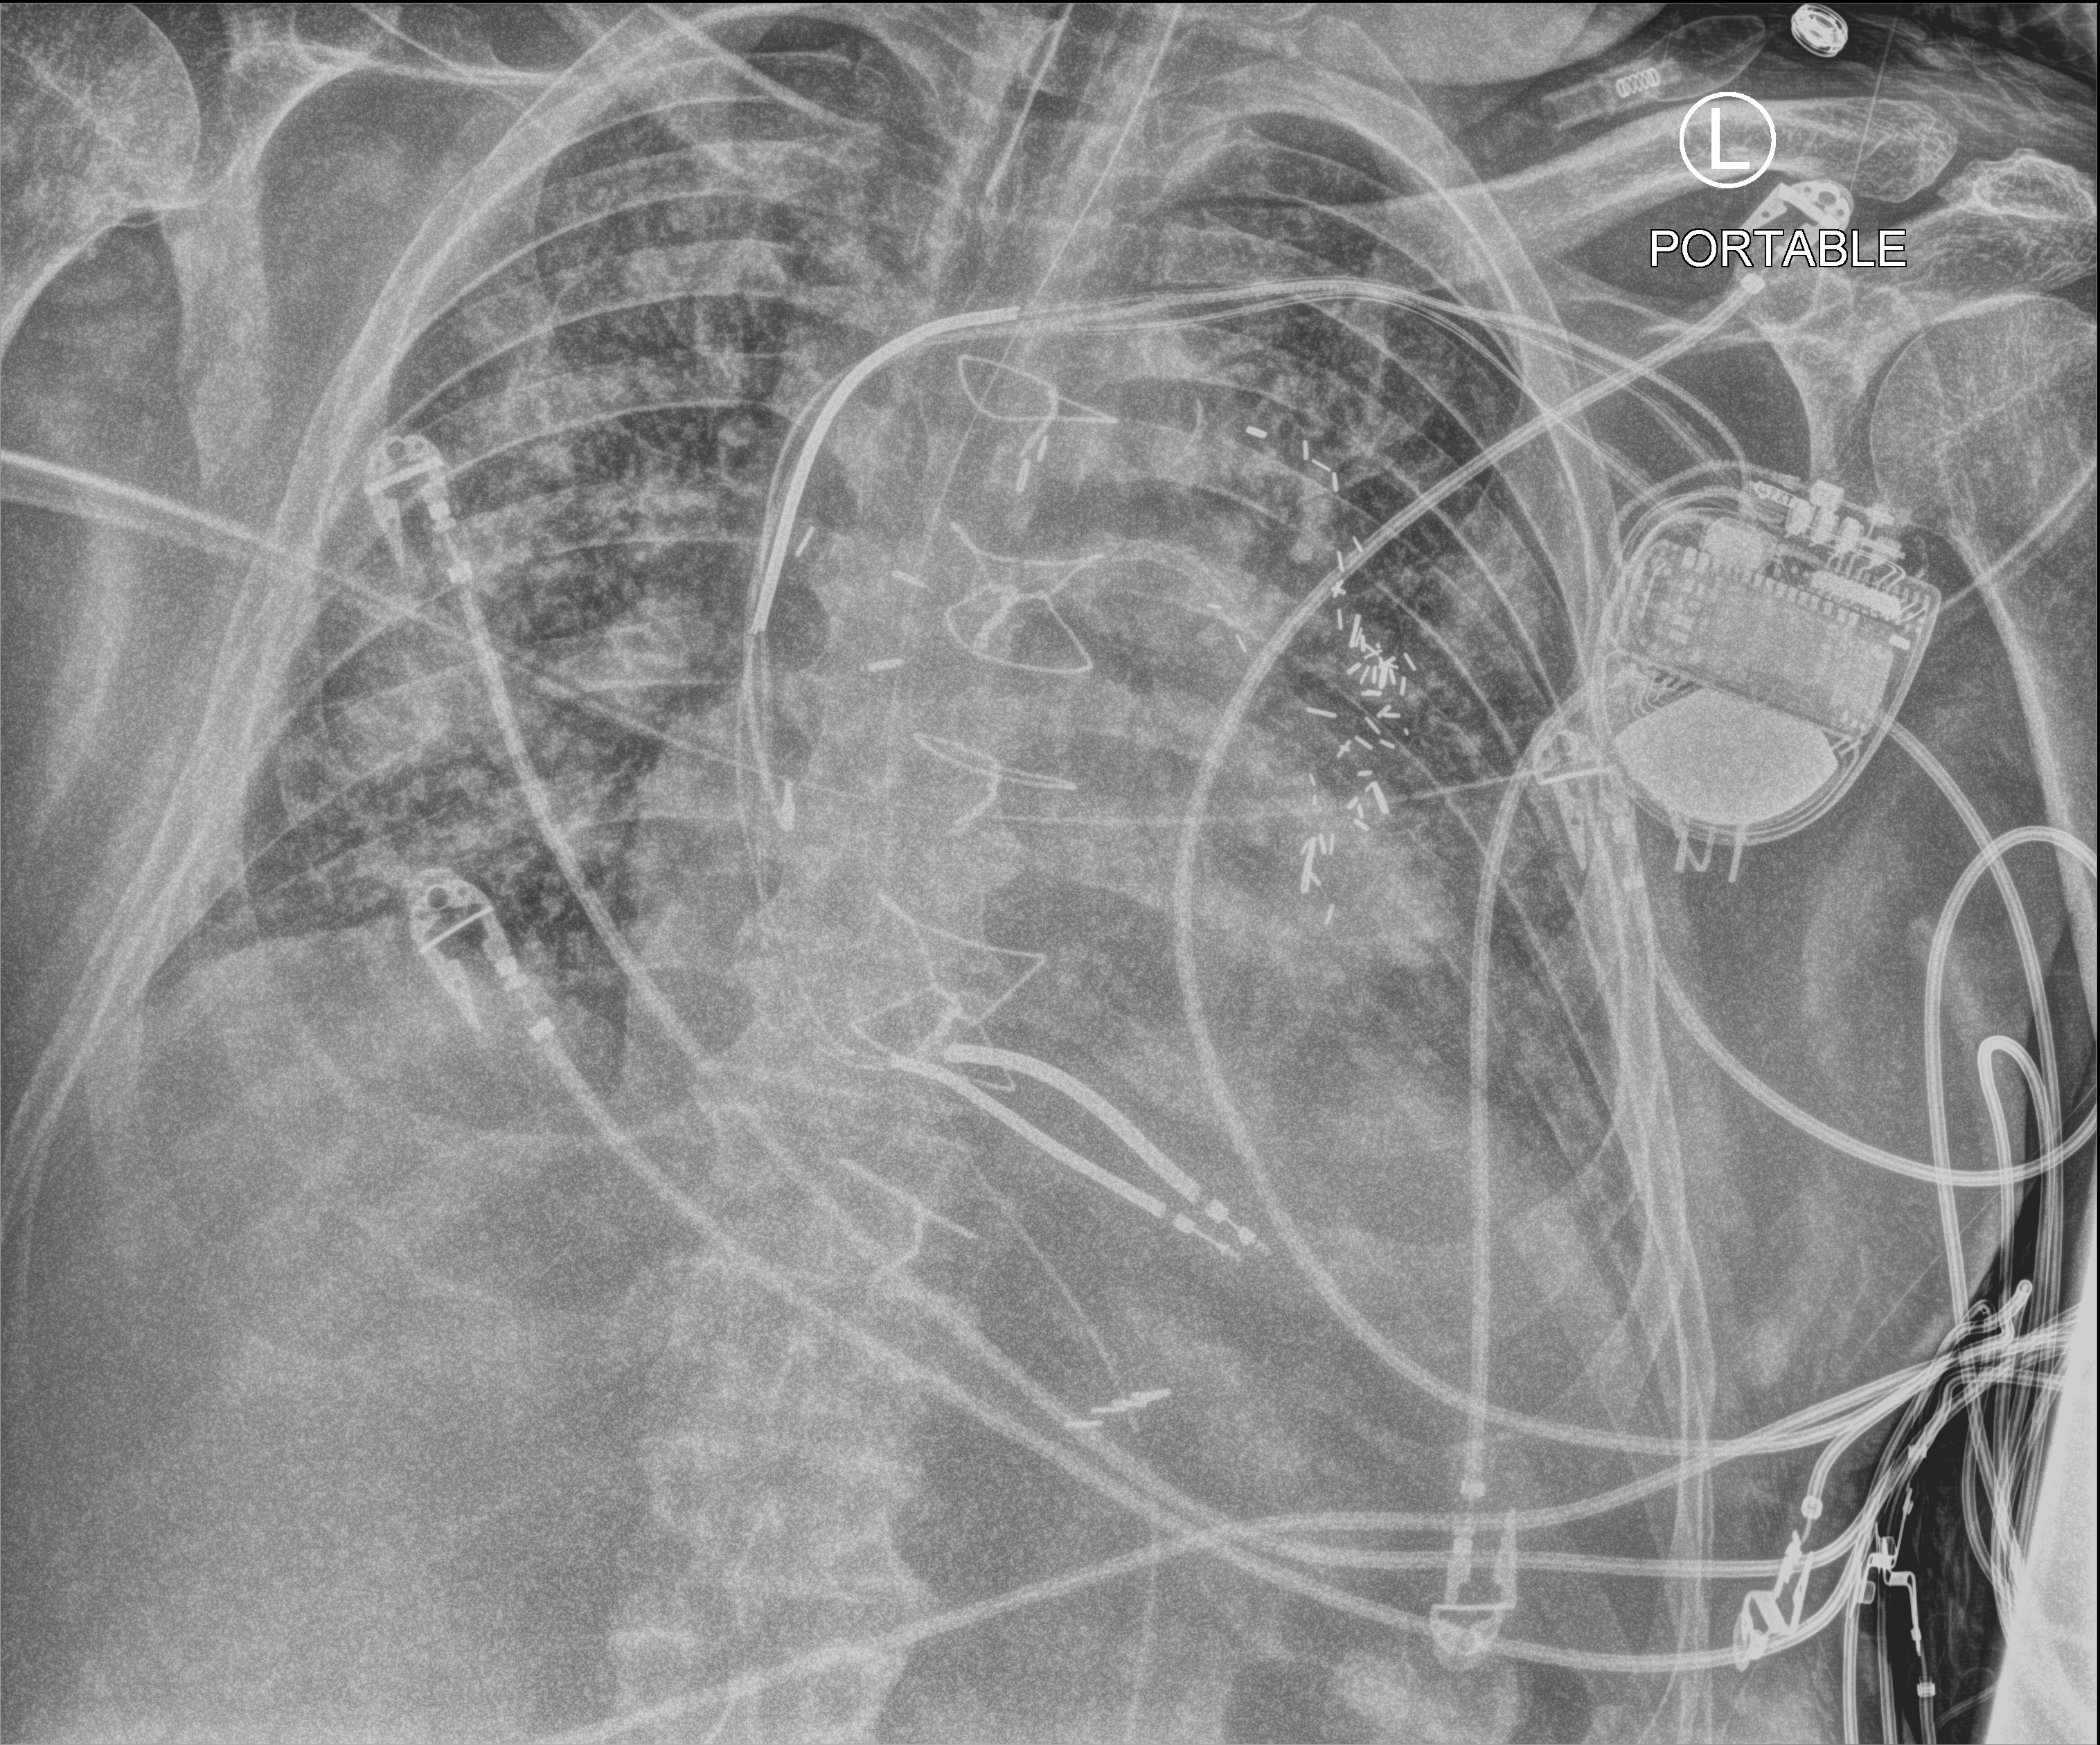
Bedside chest radiograph (computed radiography); anteroposterior (AP) projection. Patient hospitalised with COVID-19; male, aged 60–74 years.
Admission-level facts for this patient (not findings on this image; timing relative to this image not recorded): chronic kidney disease (admission record): no.